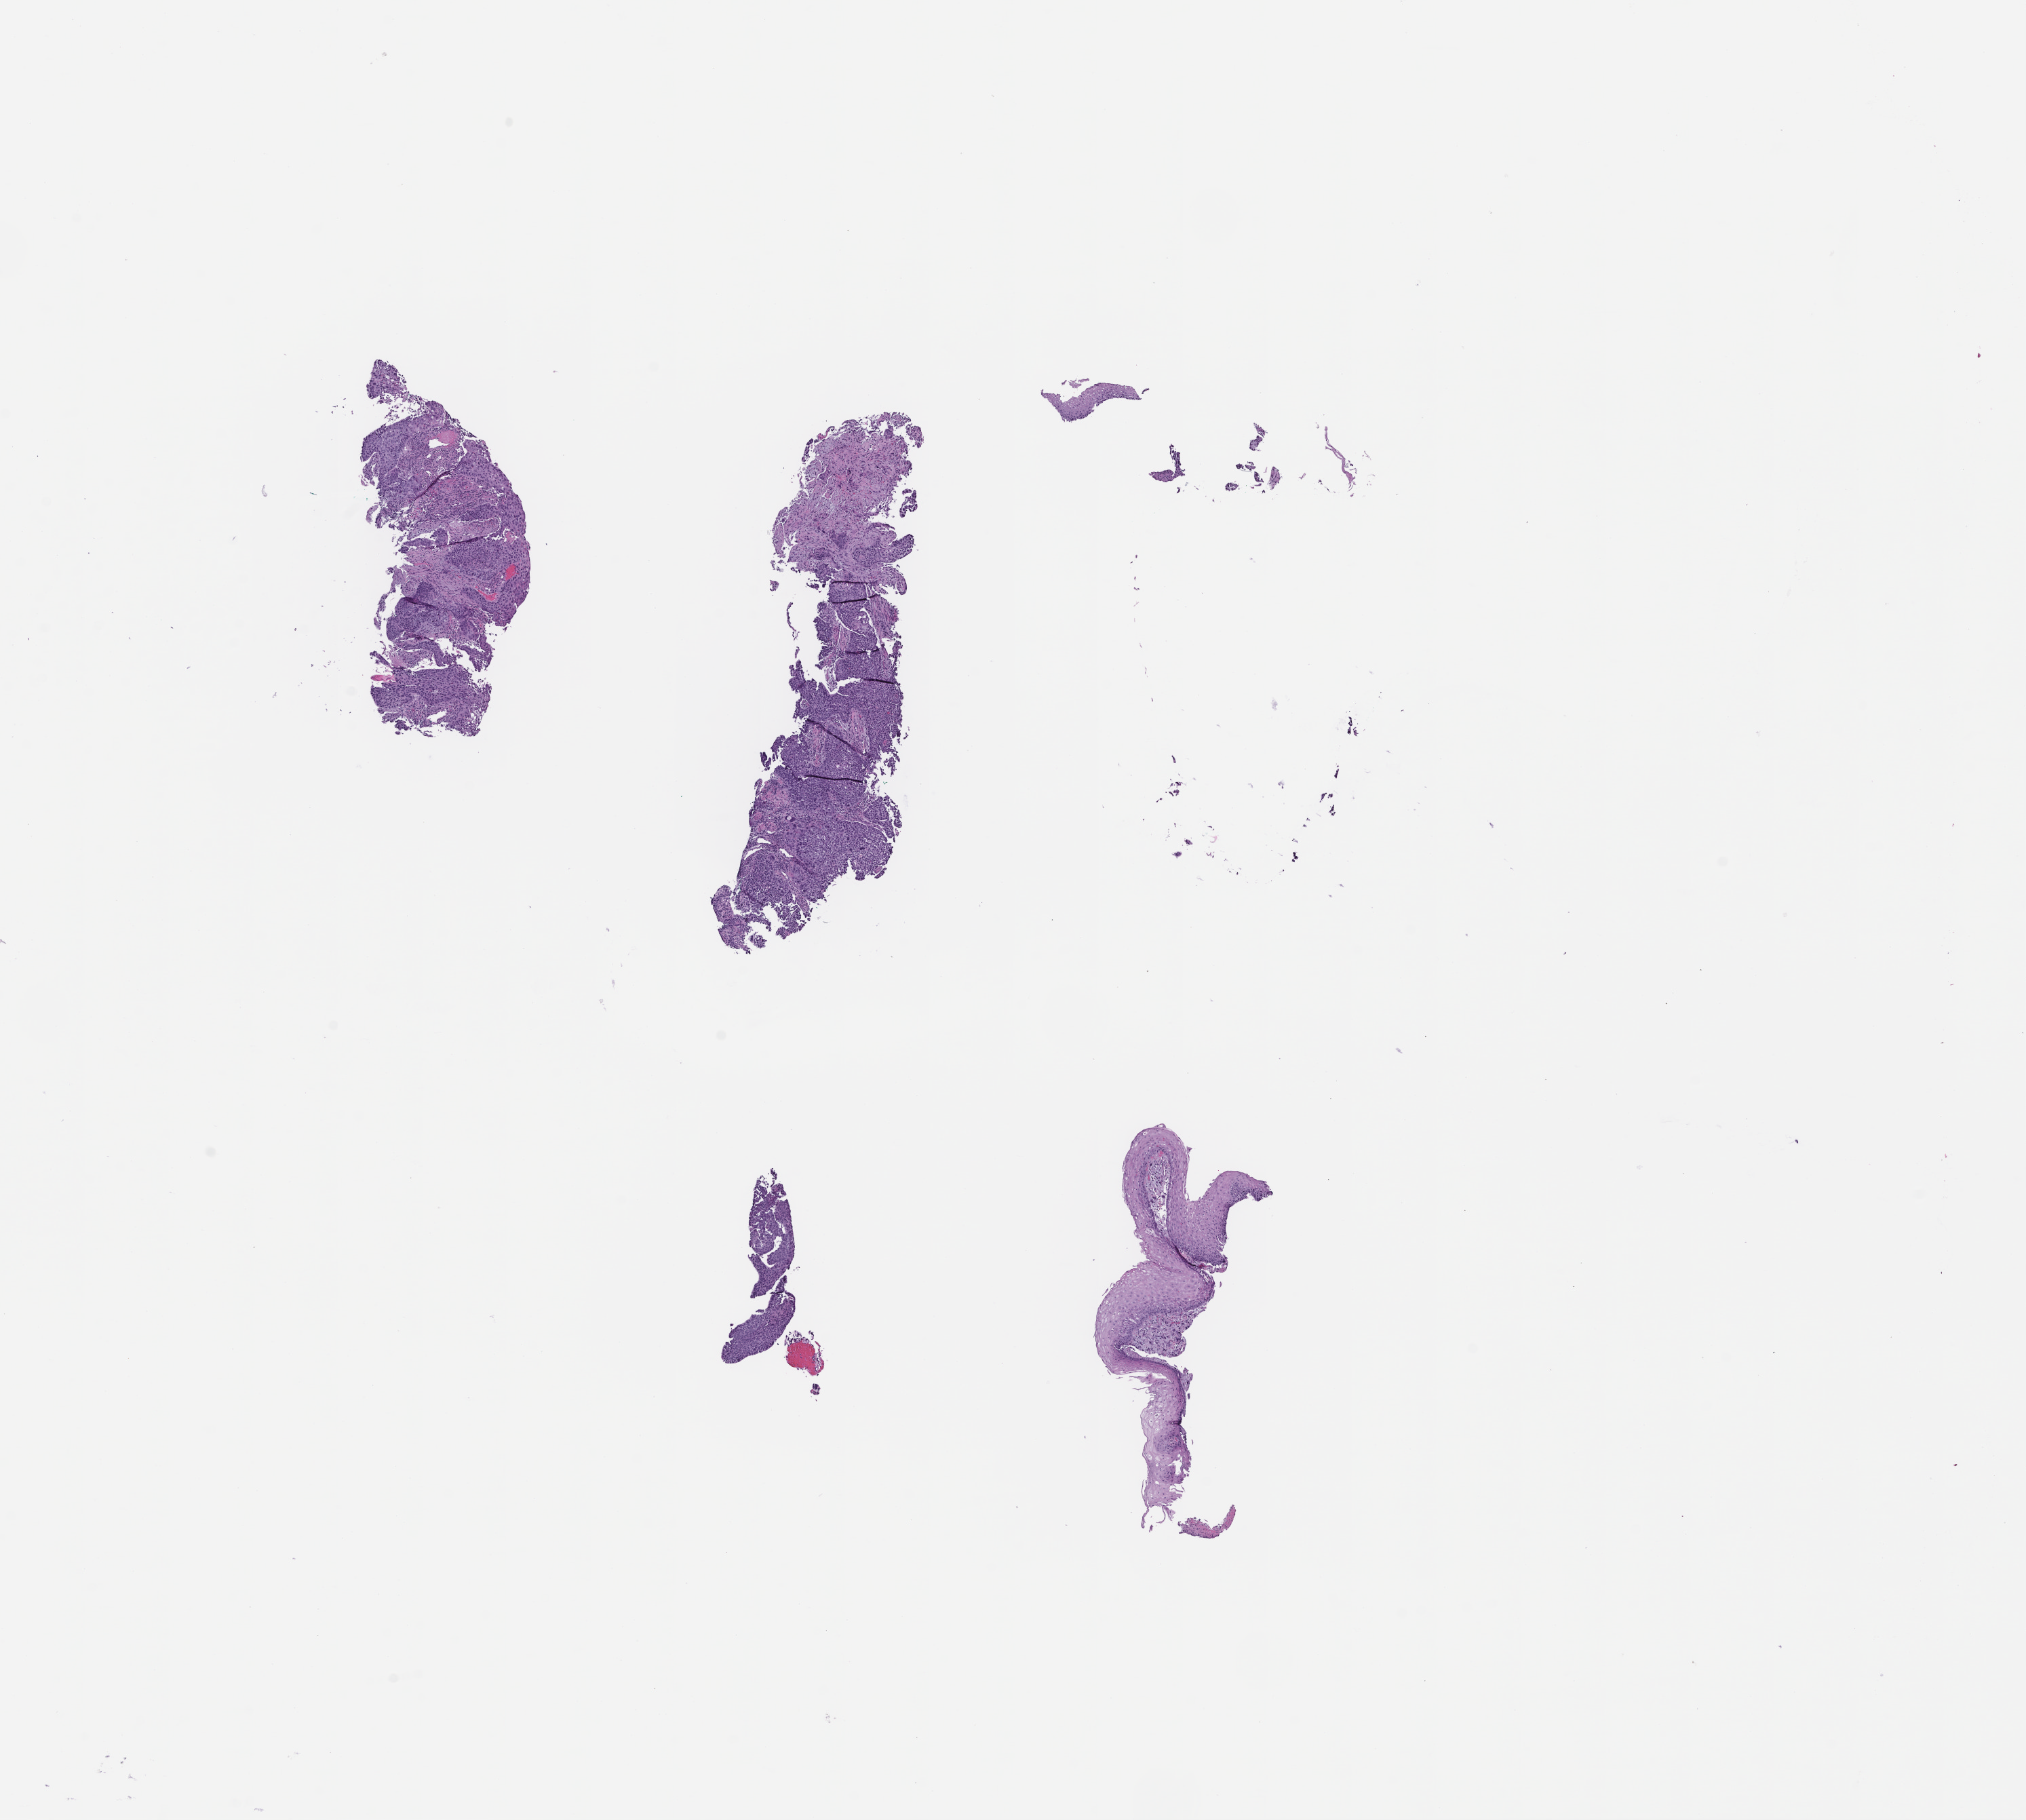
Digitized hematoxylin and eosin (H&E)-stained section, whole scanned area (about 12.1 x 10.8 mm) shown as a low-resolution overview; paraffin-embedded section (EDTA recorded as fixative); archival tissue. Patient: female.
This section: metastatic tumor tissue. Patient diagnosis (primary): Esophageal Carcinoma.